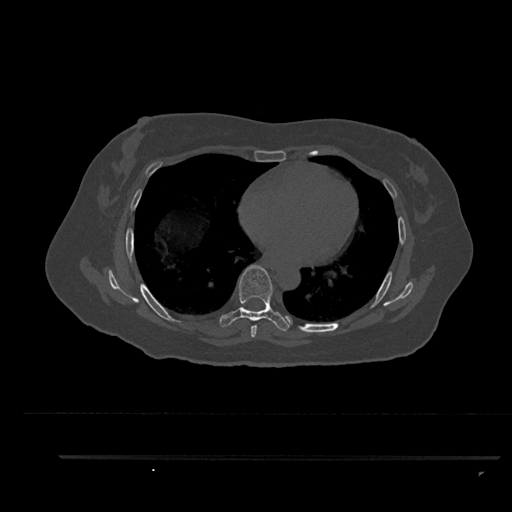
CT including the spine, one axial slice; slice 515 of 797 in the series (ordered by position); reconstruction kernel Br40s/3; 120 kVp; bone window (W 1800 / L 400 HU); 0.5 mm slice thickness; 512 × 512 image matrix, field of view 408 × 408 mm. Female patient, age 44 years. Case-level facts recorded for this patient, not image findings: primary cancer: renal.
Outlined on this slice (semi-automatic segmentation, software-assisted and operator-edited):
- T6 vertebra: bounding box (x1, y1, x2, y2) in pixels: (251, 320, 257, 337)
- T7 vertebra: (219, 265, 292, 331)